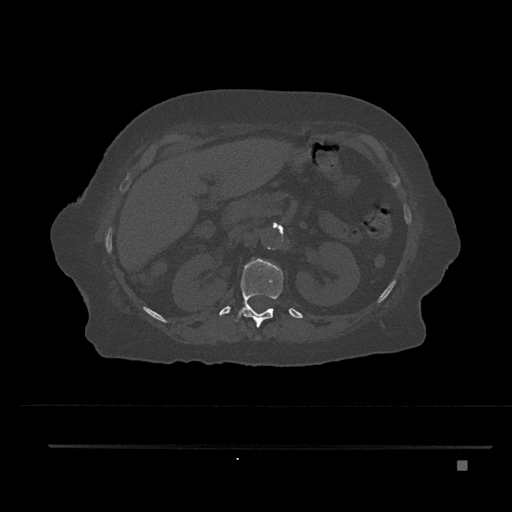
CT including the spine, one axial slice. Slice 258 of 797 in the series (ordered by position). 120 kVp. Bone window (W 1800 / L 400 HU). 0.5 mm slice thickness. 512 × 512 image matrix, field of view 437 × 437 mm. Female patient, age 76 years. From the clinical record (not read from this slice): primary cancer: lung; vertebrae with lytic lesions (as recorded): T11, L3.
Outlined on this slice (semi-automatically segmented with operator editing):
- L1 vertebra: bounding box <253,258,258,260> (left, top, right, bottom; pixels)
- T12 vertebra: <235,258,283,328>